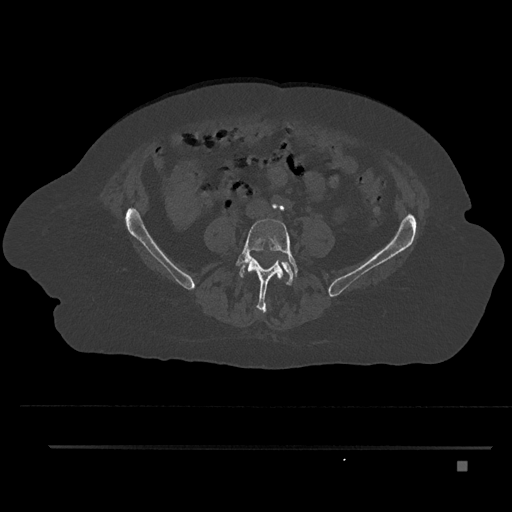
CT including the spine, one axial slice; position 77 of 797 along the scan axis; reconstruction kernel Br40s/3; 120 kVp; bone window (W 1800 / L 400 HU); 0.5 mm slice thickness; 512 × 512 image matrix, field of view 437 × 437 mm. Female patient, age 76 years. From the clinical record (not read from this slice): primary cancer: lung.
Structures marked on this image (semi-automatically segmented with operator editing):
- L3 vertebra: bounding box (x1, y1, x2, y2) in pixels: (279, 273, 281, 276)
- L4 vertebra: (235, 218, 298, 312)
- L5 vertebra: (240, 261, 297, 285)